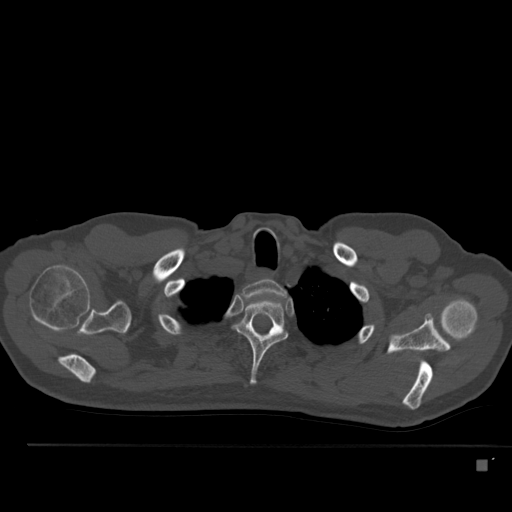
CT including the spine, one axial slice; position 412 of 517 along the scan axis; 120 kVp; bone window (W 1800 / L 400 HU); 1.5 mm slice thickness; 512 × 512 image matrix, field of view 408 × 408 mm. Patient: male, 70 years. From the clinical record (not read from this slice): primary cancer: renal; vertebrae with lytic lesions (as recorded): T4, T6, T10, T12, L3, L4, L5.
Structures marked on this image (semi-automatic segmentation, software-assisted and operator-edited):
- T1 vertebra: bounding box (x1, y1, x2, y2) in pixels: (242, 279, 286, 297)
- T2 vertebra: (236, 299, 288, 385)
- T3 vertebra: (272, 325, 274, 328)